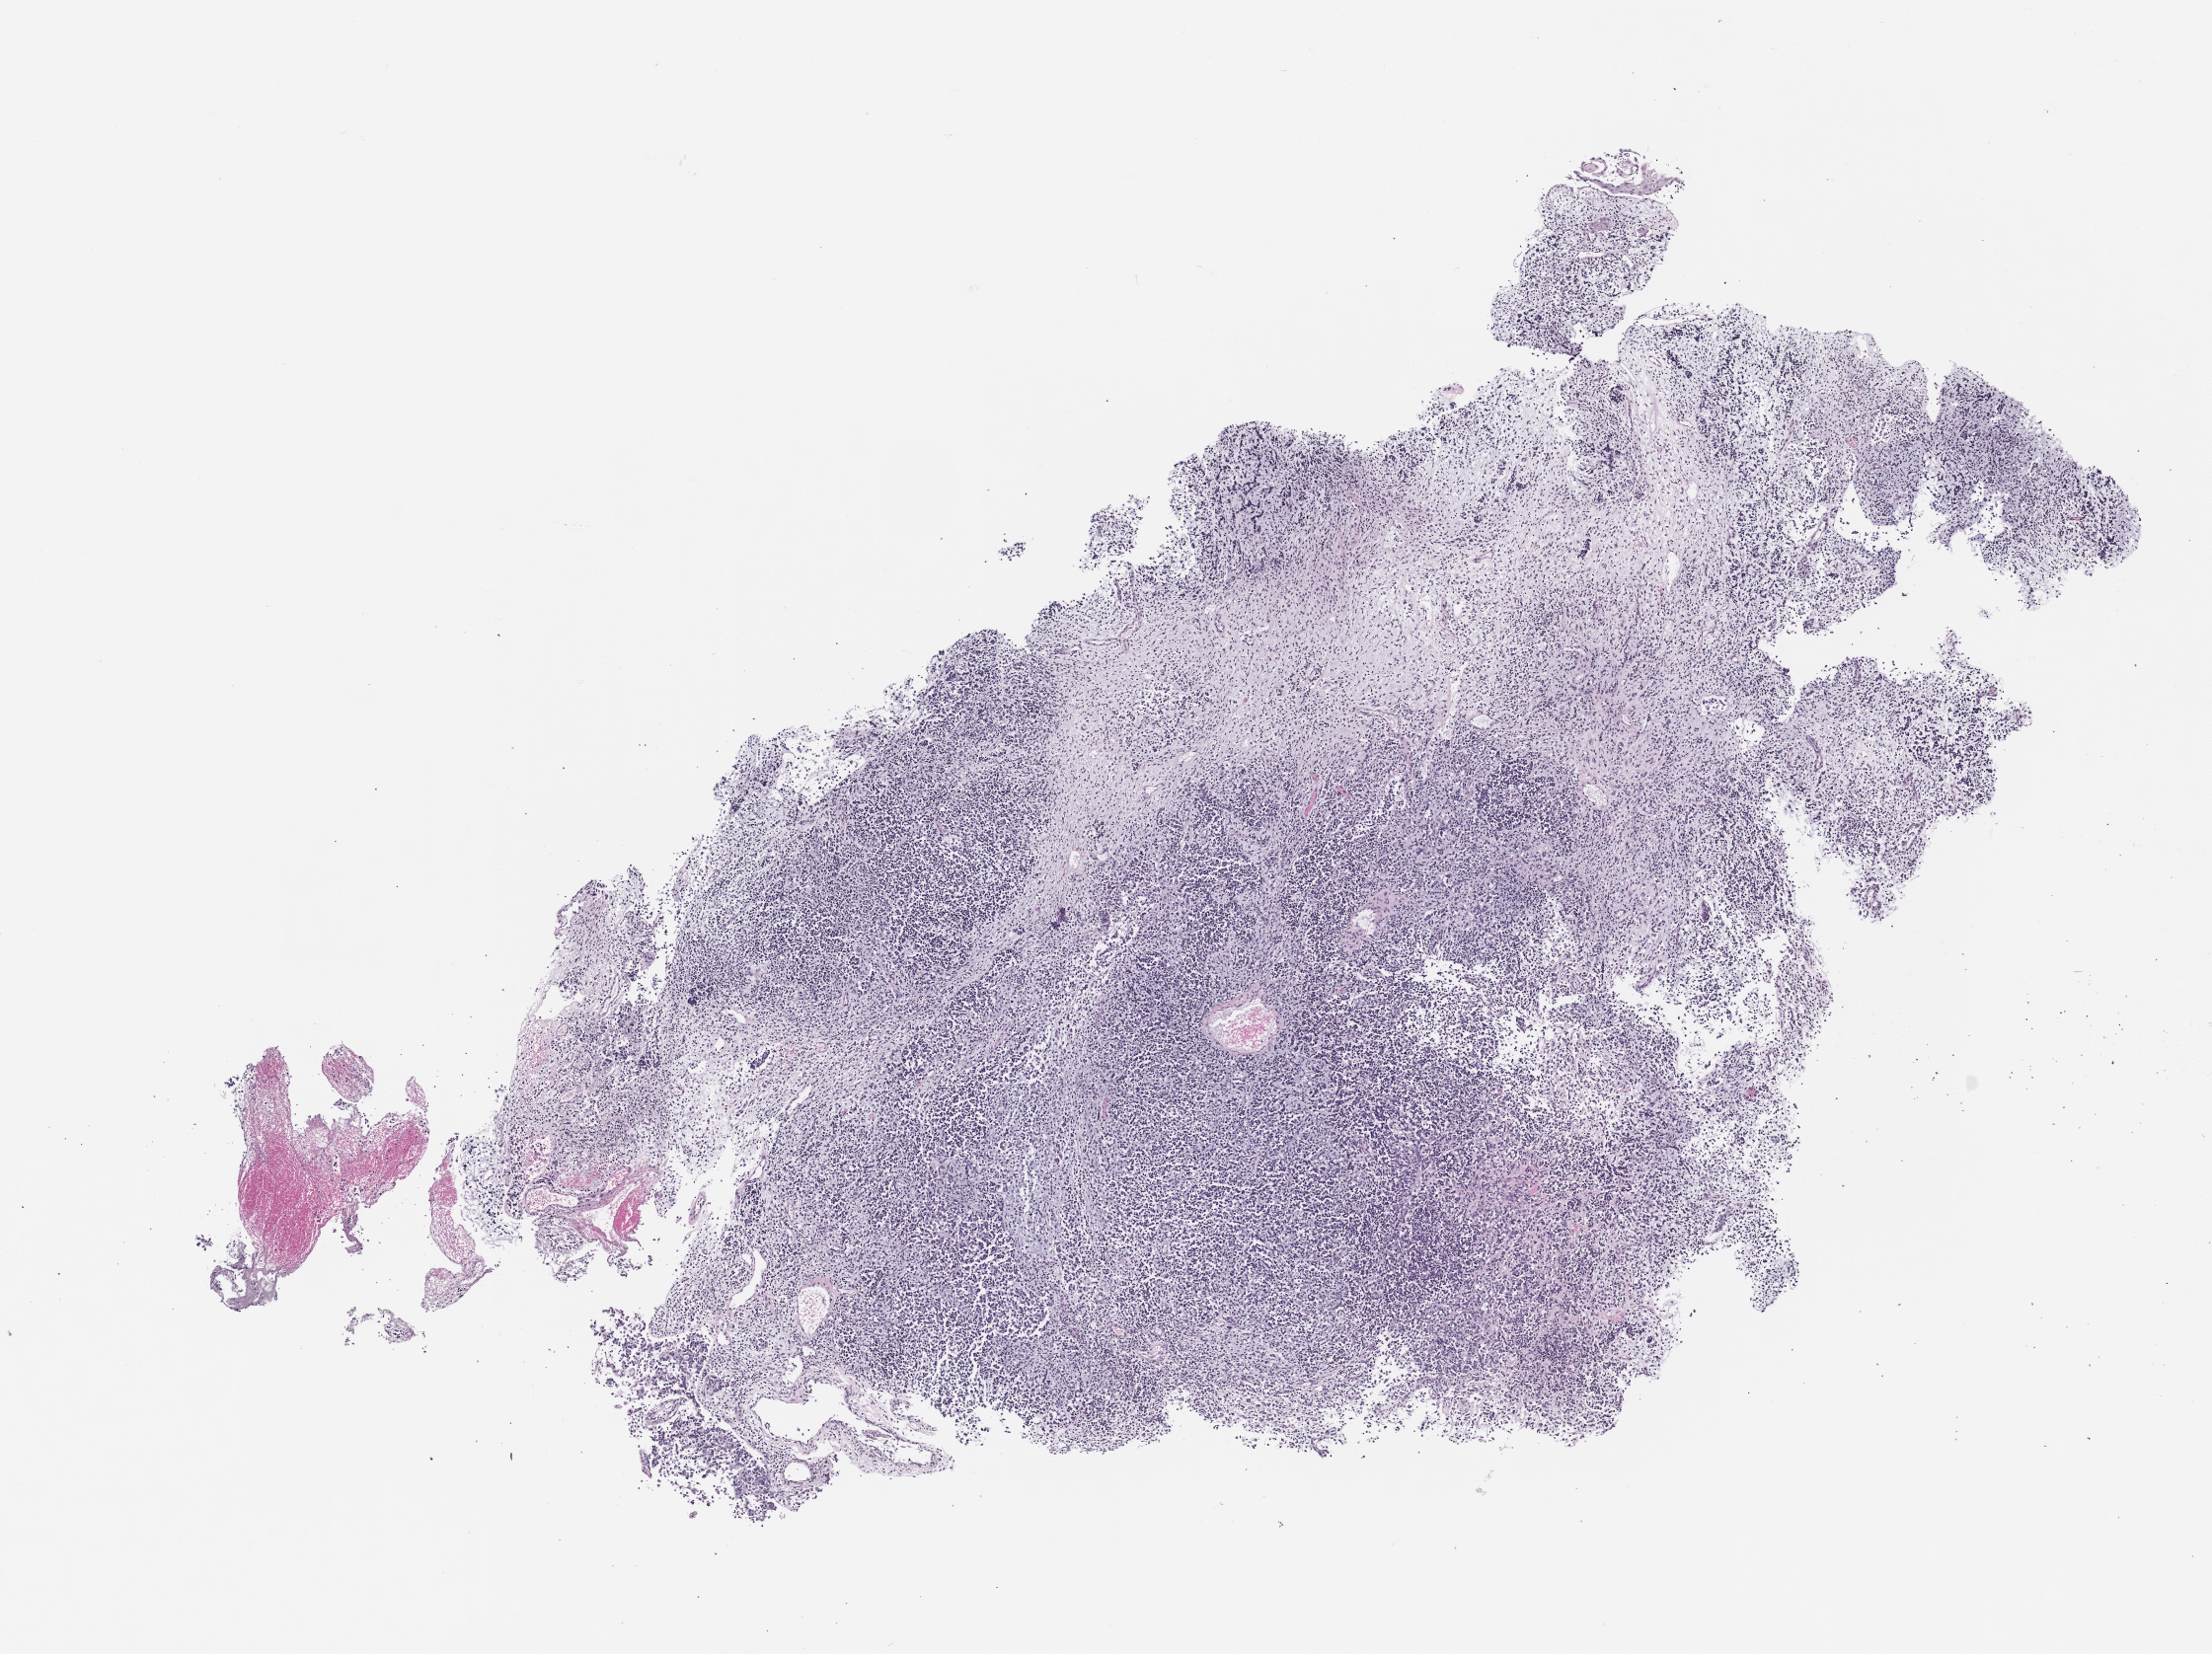
H&E whole-slide image of the patient's (originator) tumor tissue — shown as a low-resolution overview of the whole scanned area (about 9.0 x 6.7 mm), FFPE section, tumor site category: uterus. Female patient, 70 years old.
Diagnosis: Carcinosarcoma.